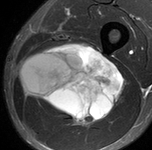
MRI of an extremity soft-tissue mass, one axial slice; slice 54 of 90 in the series (ordered by position); STIR; MR volume resampled by the dataset authors to the PET/CT grid (not the native acquisition matrix); 3.27 mm slice thickness; 152 × 150 image matrix. Male patient. Case-level facts recorded for this patient, not image findings: histological type: undifferentiated pleomorphic liposarcoma; grade: high; site of the primary tumour: left thigh.
Structures marked on this image (expert contour drawn on MRI and transferred to this co-registered scan by the dataset authors):
- gross tumour volume including surrounding oedema: bounding box <18,43,124,127> (left, top, right, bottom; pixels)
- gross tumour volume (mass): <20,43,124,127>